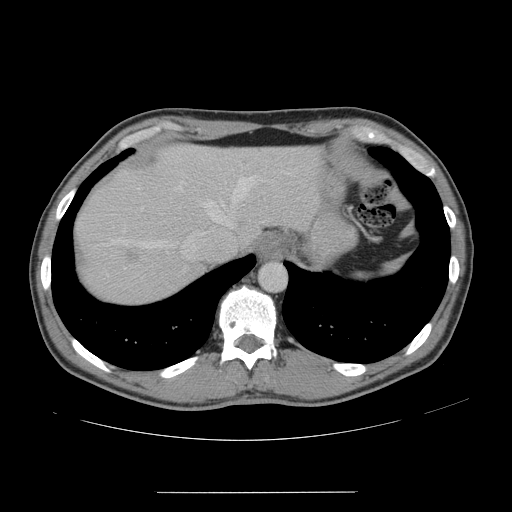
Contrast-enhanced abdominal CT, one axial slice; position 127 of 178 along the scan axis; intravenous contrast given; soft-tissue window (W 400 / L 40 HU); 2.5 mm slice thickness; 512 × 512 image matrix. Male patient, age 53 years. Case-level facts recorded for this patient, not image findings: diagnosis: colorectal cancer liver metastases, imaged before liver resection; multiple liver metastases: yes; largest metastasis: 2.4 cm; disease in both lobes: no.
Structures marked on this image (outlined manually by an expert reader):
- hepatic veins: bounding box [x1, y1, x2, y2] px = [112, 177, 254, 259]
- liver: [77, 145, 317, 304]
- planned liver remnant (the part of the liver to remain after resection): [161, 145, 317, 241]
- liver metastasis: [125, 250, 138, 259]